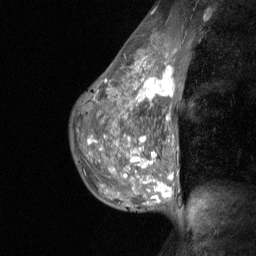
Breast MRI (dynamic contrast-enhanced), one sagittal slice; position 40 of 64 along the scan axis; dynamic contrast-enhanced study with each time point stored as its own series, time point 2 of 3 at this slice position (early post-contrast, ordered by acquisition time); 1.5 T; TE 4.8 ms, TR 27 ms; 2 mm slice thickness; 256 × 256 image matrix. Female patient, age 36 years. From the clinical record (not read from this slice): setting: breast cancer imaged before/during neoadjuvant chemotherapy; receptor status: HR-positive, HER2-negative.
Outlined on this slice (semi-automatically segmented with operator editing):
- analysis volume of interest (the breast-tissue region the enhancement analysis was run in; not a lesion): bounding box [x1, y1, x2, y2] px = [73, 45, 184, 210]
- tumour enhancement mask (voxels above the 90 % enhancement threshold inside the analysis volume of interest): [88, 66, 175, 202]